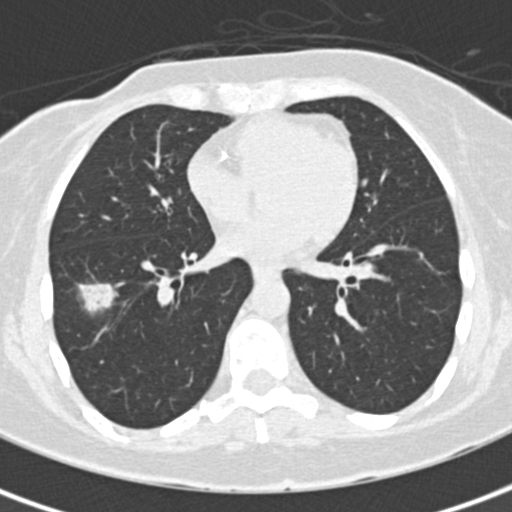
Low-dose screening chest CT, one axial slice; slice 76 of 171 in the series (ordered by position); reconstruction kernel B30f; lung window (W 1500 / L -600 HU); 512 × 512 image matrix, field of view 284 × 284 mm.
Outlined on this slice (expert manual segmentation):
- lesion 1 (tumor, lower lobe of right lung): bounding box <78,283,118,314> (left, top, right, bottom; pixels)